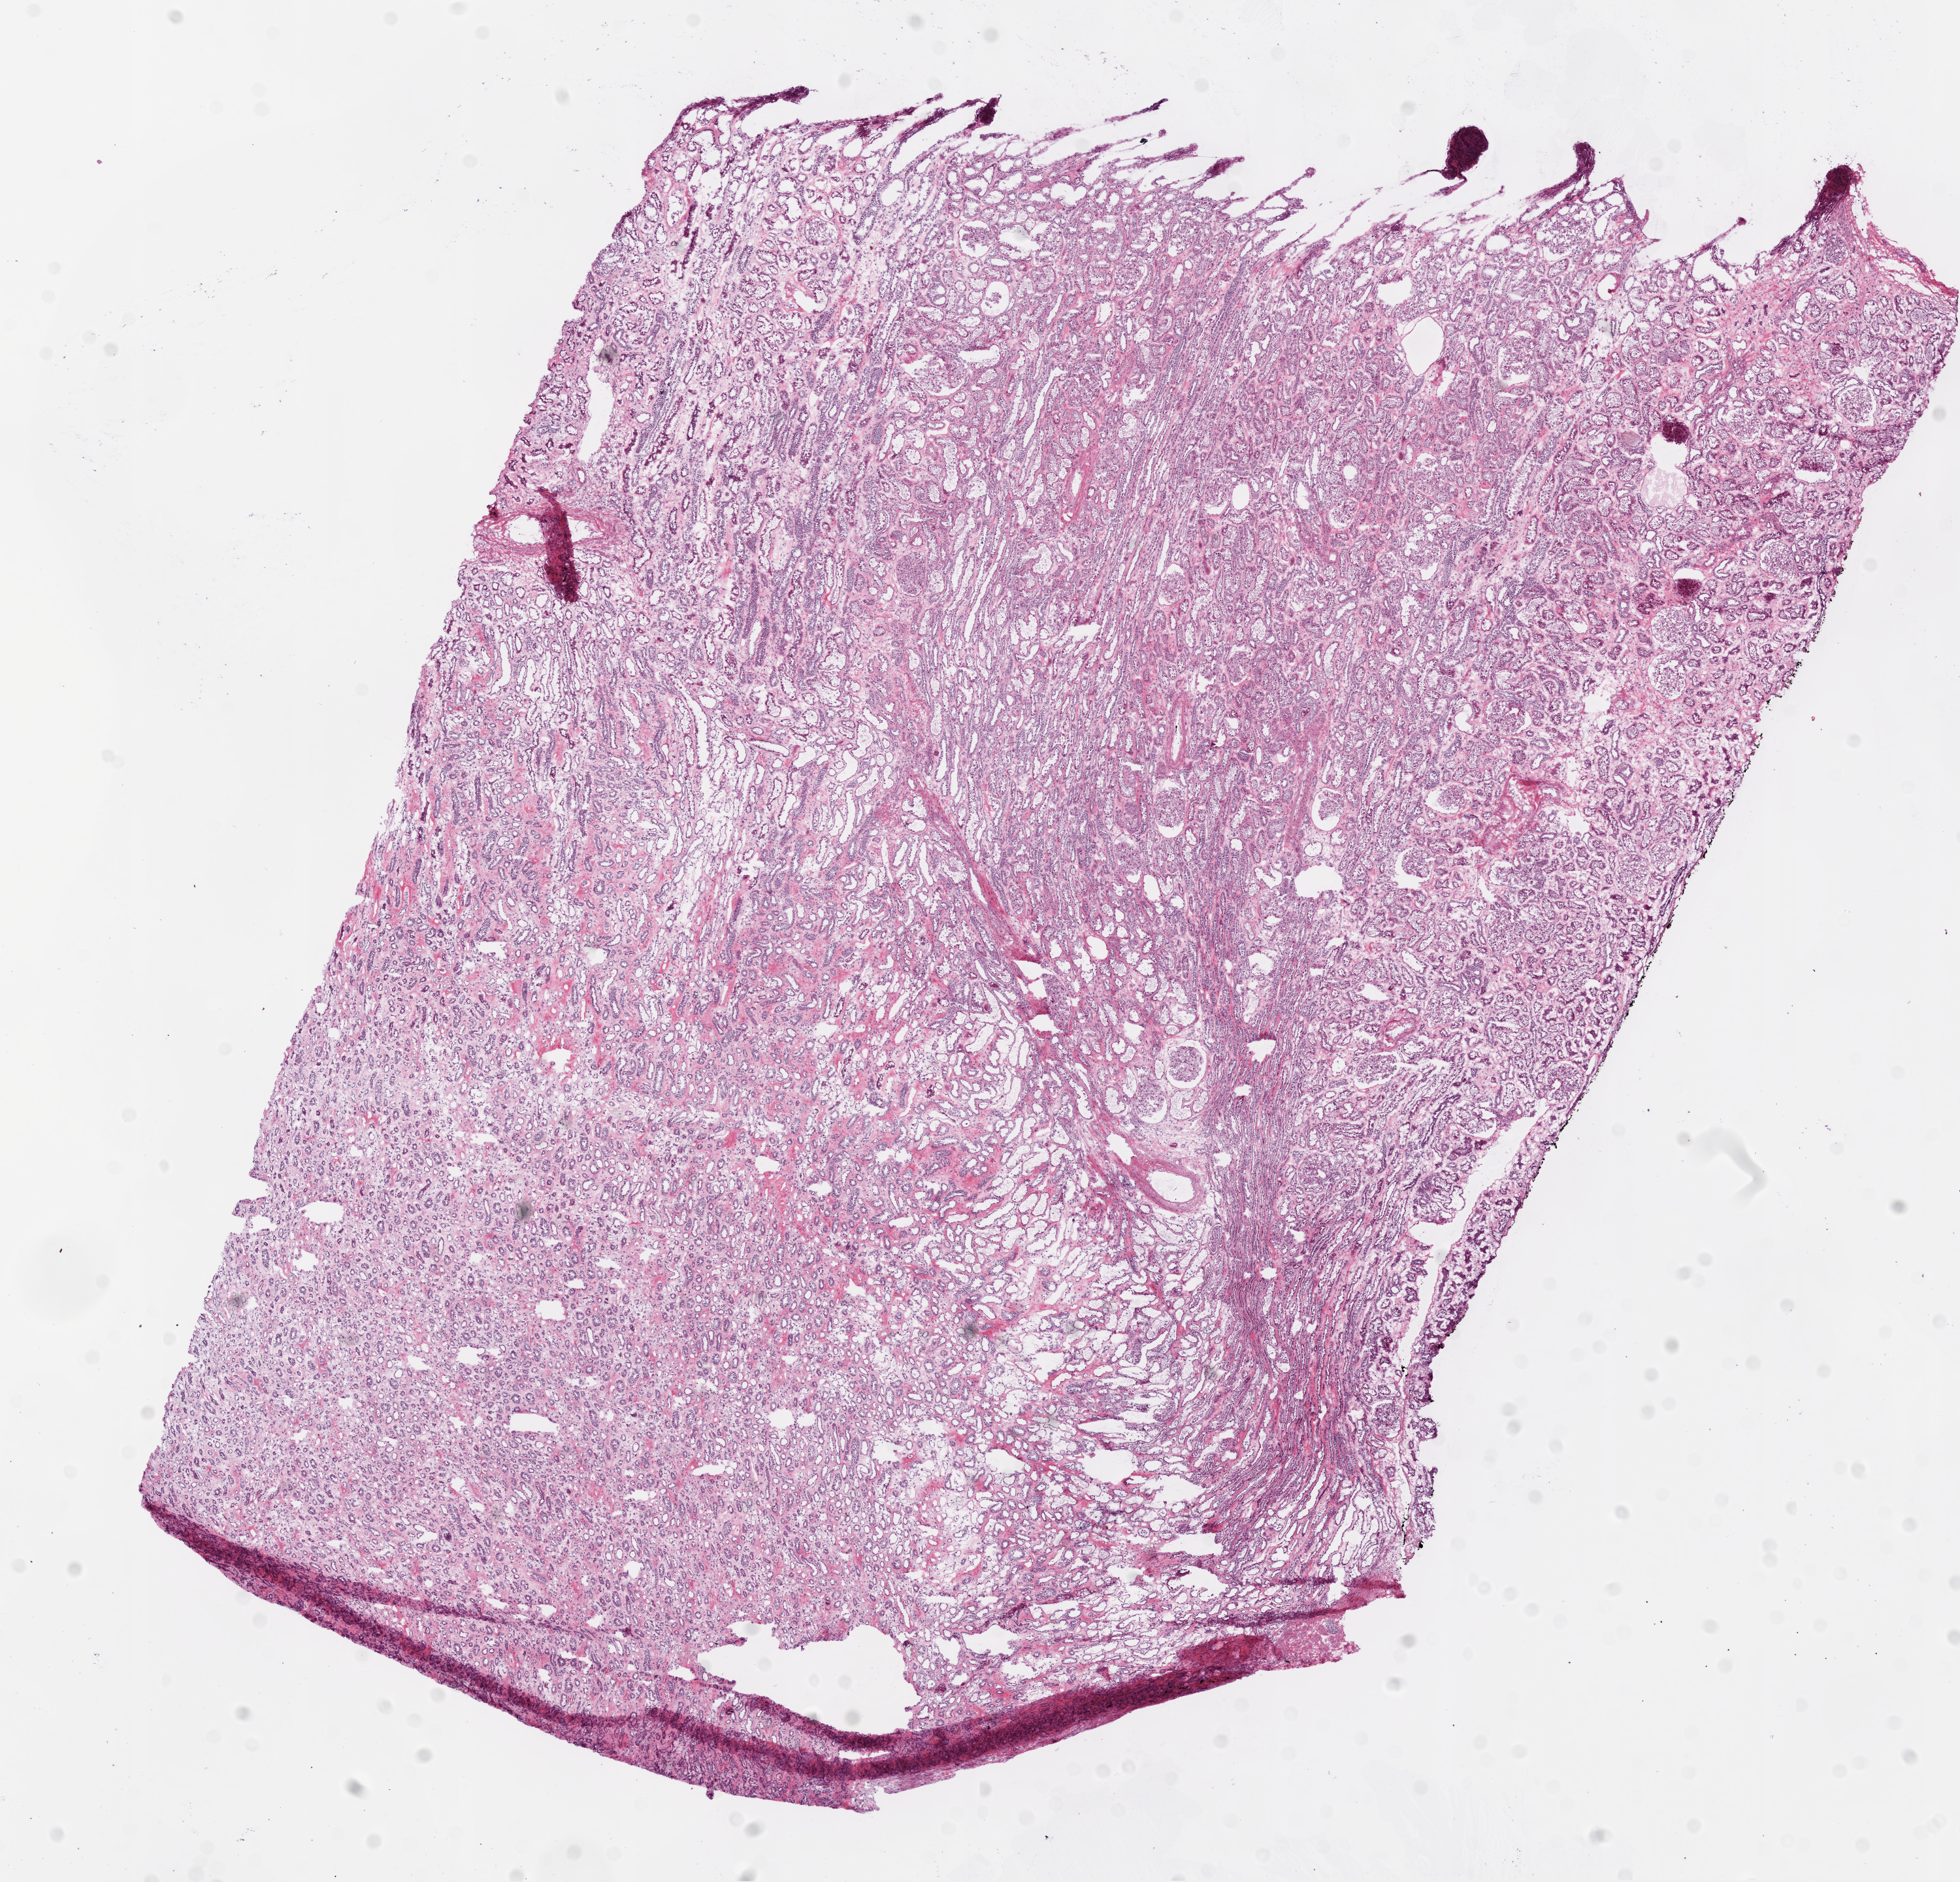
Digitized Hematoxylin and eosin (H&E) stained tissue section (whole slide), whole scanned area (about 12.0 x 11.6 mm, slide scanned at 20x) shown as a low-resolution overview. Frozen section from the bottom of the tissue portion. Sample: solid tissue normal (non-tumour tissue), kidney. Patient: male, age at initial diagnosis 67 years.
This section: solid tissue normal sample (biorepository sample class). Patient diagnosis: Clear cell adenocarcinoma, NOS.